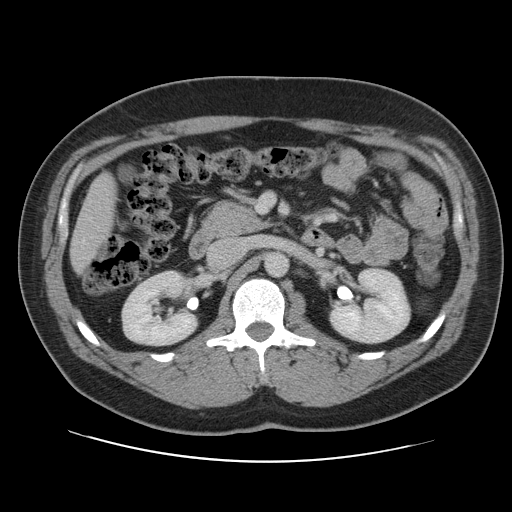
Contrast-enhanced abdominal CT, one axial slice. Intravenous contrast given. Soft-tissue window (W 400 / L 40 HU). 512 × 512 image matrix, field of view 402 × 402 mm. Male patient, age 35 years. Case-level facts recorded for this patient, not image findings: diagnosis: colorectal cancer liver metastases, imaged before liver resection; multiple liver metastases: yes; largest metastasis: 2.8 cm; chemotherapy before resection: yes.
Outlined on this slice (manually delineated by an expert):
- liver: bounding box <72,177,115,270> (left, top, right, bottom; pixels)
- planned liver remnant (the part of the liver to remain after resection): <72,176,115,270>